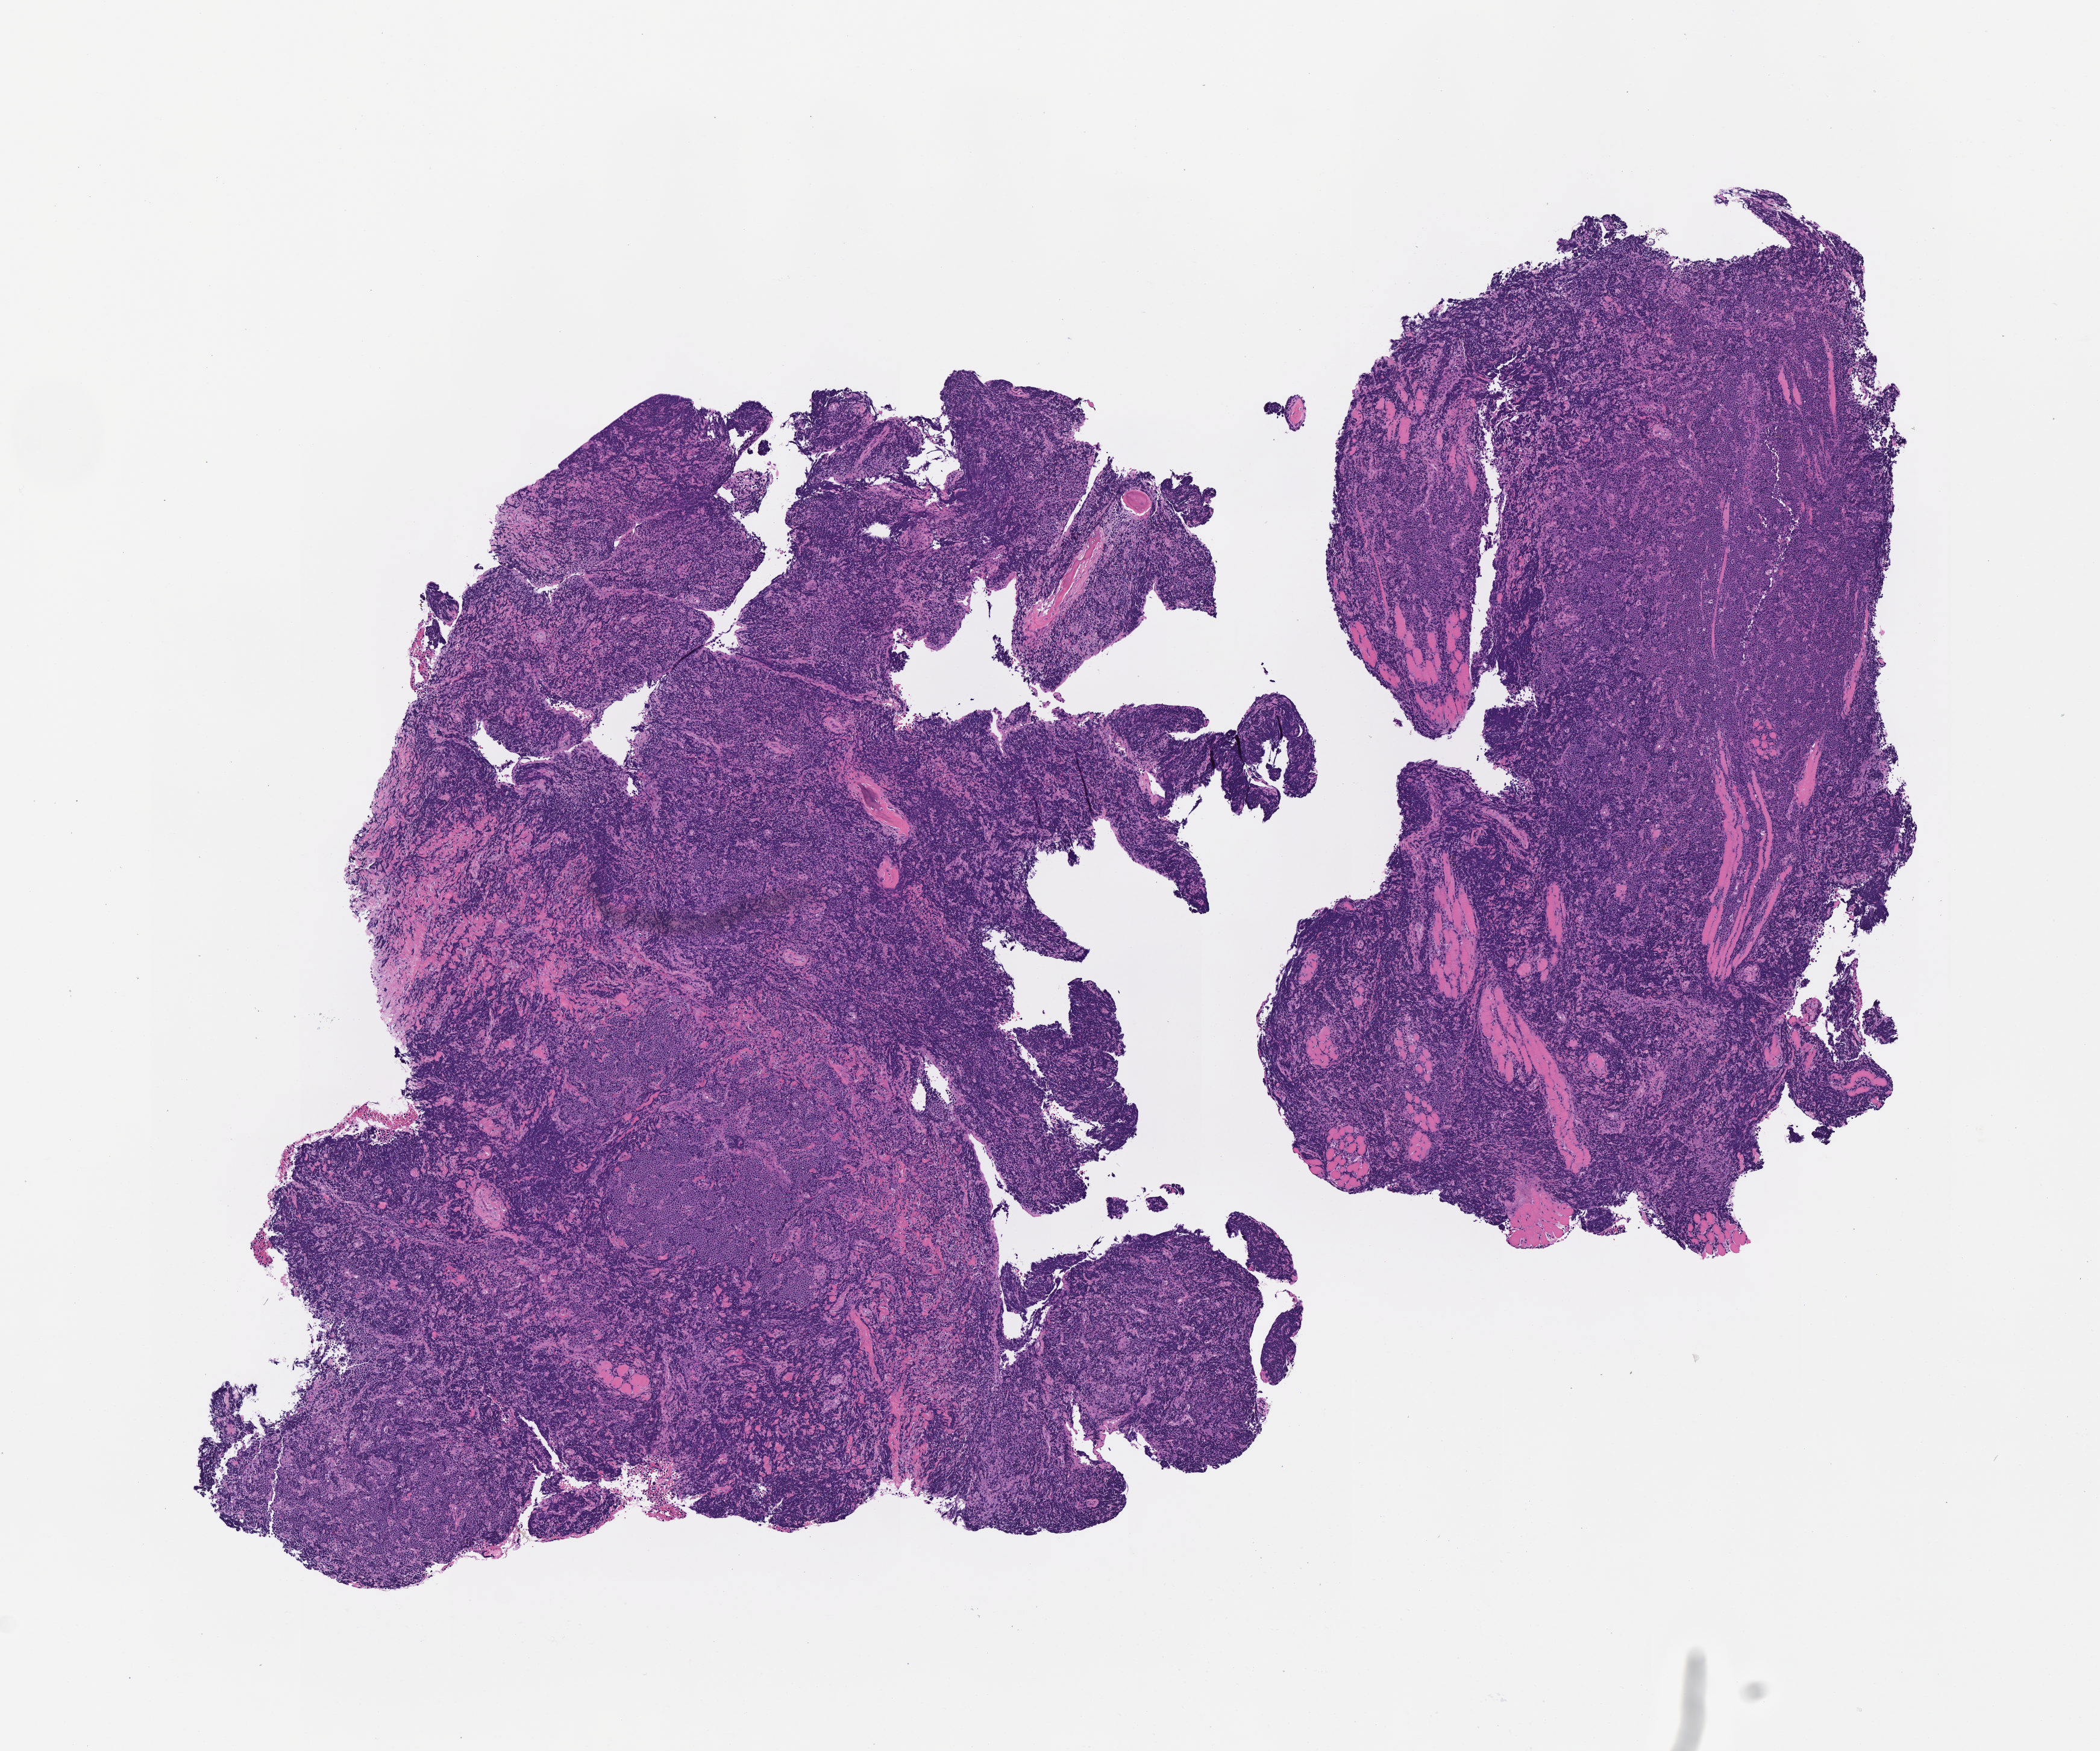
Digitized H&E-stained section, whole scanned area (about 7.0 x 5.9 mm) shown as a low-resolution overview, specimen: tumor tissue, site: cranium. Patient: male, age at initial diagnosis 8 years.
Diagnosis: Burkitt lymphoma, NOS.